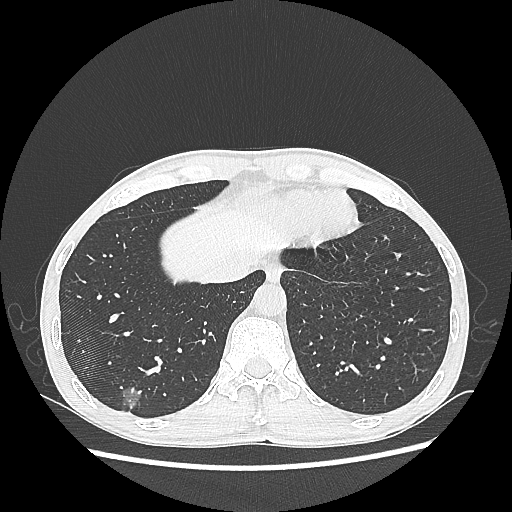
Chest CT, one axial slice; position 65 of 270 along the scan axis; 100 kVp; lung window (W 1500 / L -600 HU); 1.25 mm slice thickness; 512 × 512 image matrix, field of view 360 × 360 mm. Patient: male, 60 years. Case-level facts recorded for this patient, not image findings: clinical TNM (as recorded): T1c N0 M0; histopathological grade: G2.
Structures marked on this image (rectangle marked by the reading radiologist):
- lung tumour (recorded histology: adenocarcinoma): box from (x=113, y=384) to (x=148, y=412) px